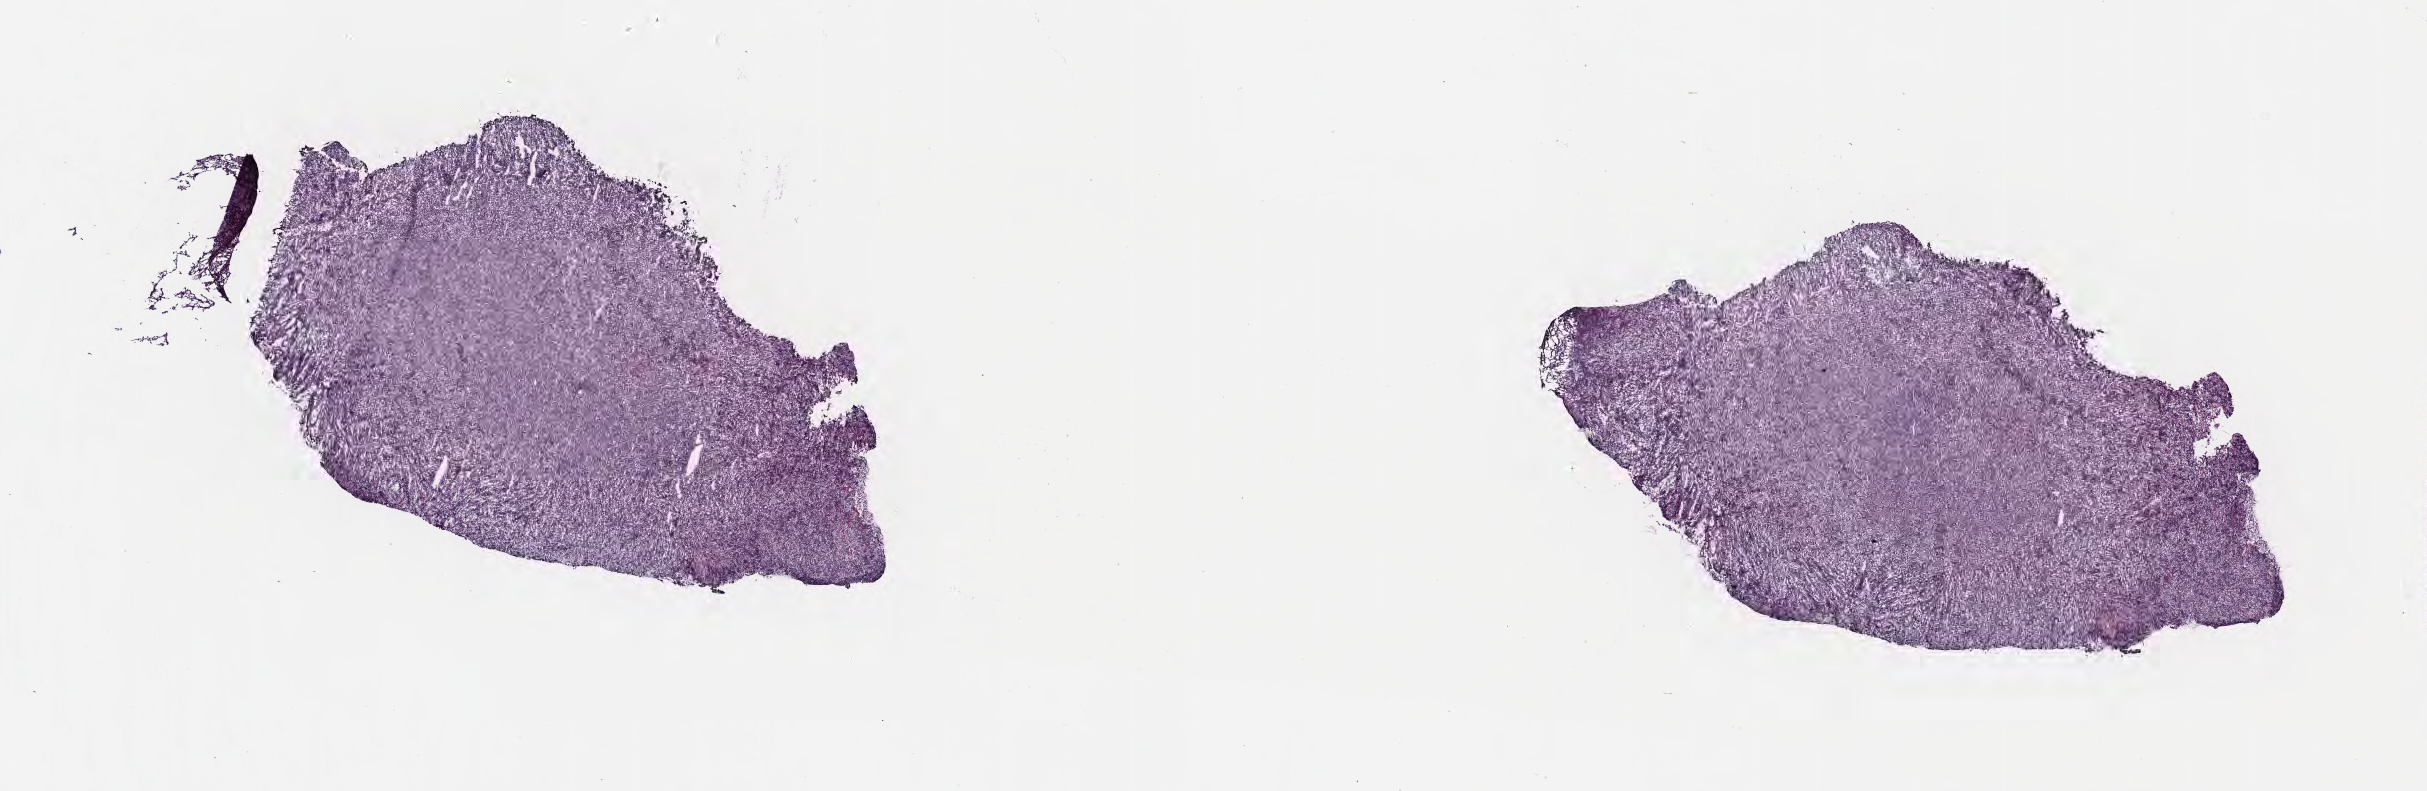
Hematoxylin and eosin (H&E) whole-slide image, low-resolution overview of the scanned area, about 19.6 x 6.4 mm, frozen section, primary tumor, anatomic site: lymph node of head and neck. Patient female; 11 years old. Slide review estimates, as recorded: tumor cells 95%, tumor nuclei 90%, stromal cells 5%, necrosis 0%, normal cells 0%. Inflammatory infiltration, as recorded: lymphocyte infiltration 40%, monocyte infiltration 30%, neutrophil infiltration 5%.
* histologic diagnosis: Burkitt lymphoma, NOS
* Ann Arbor stage (patient): Stage II